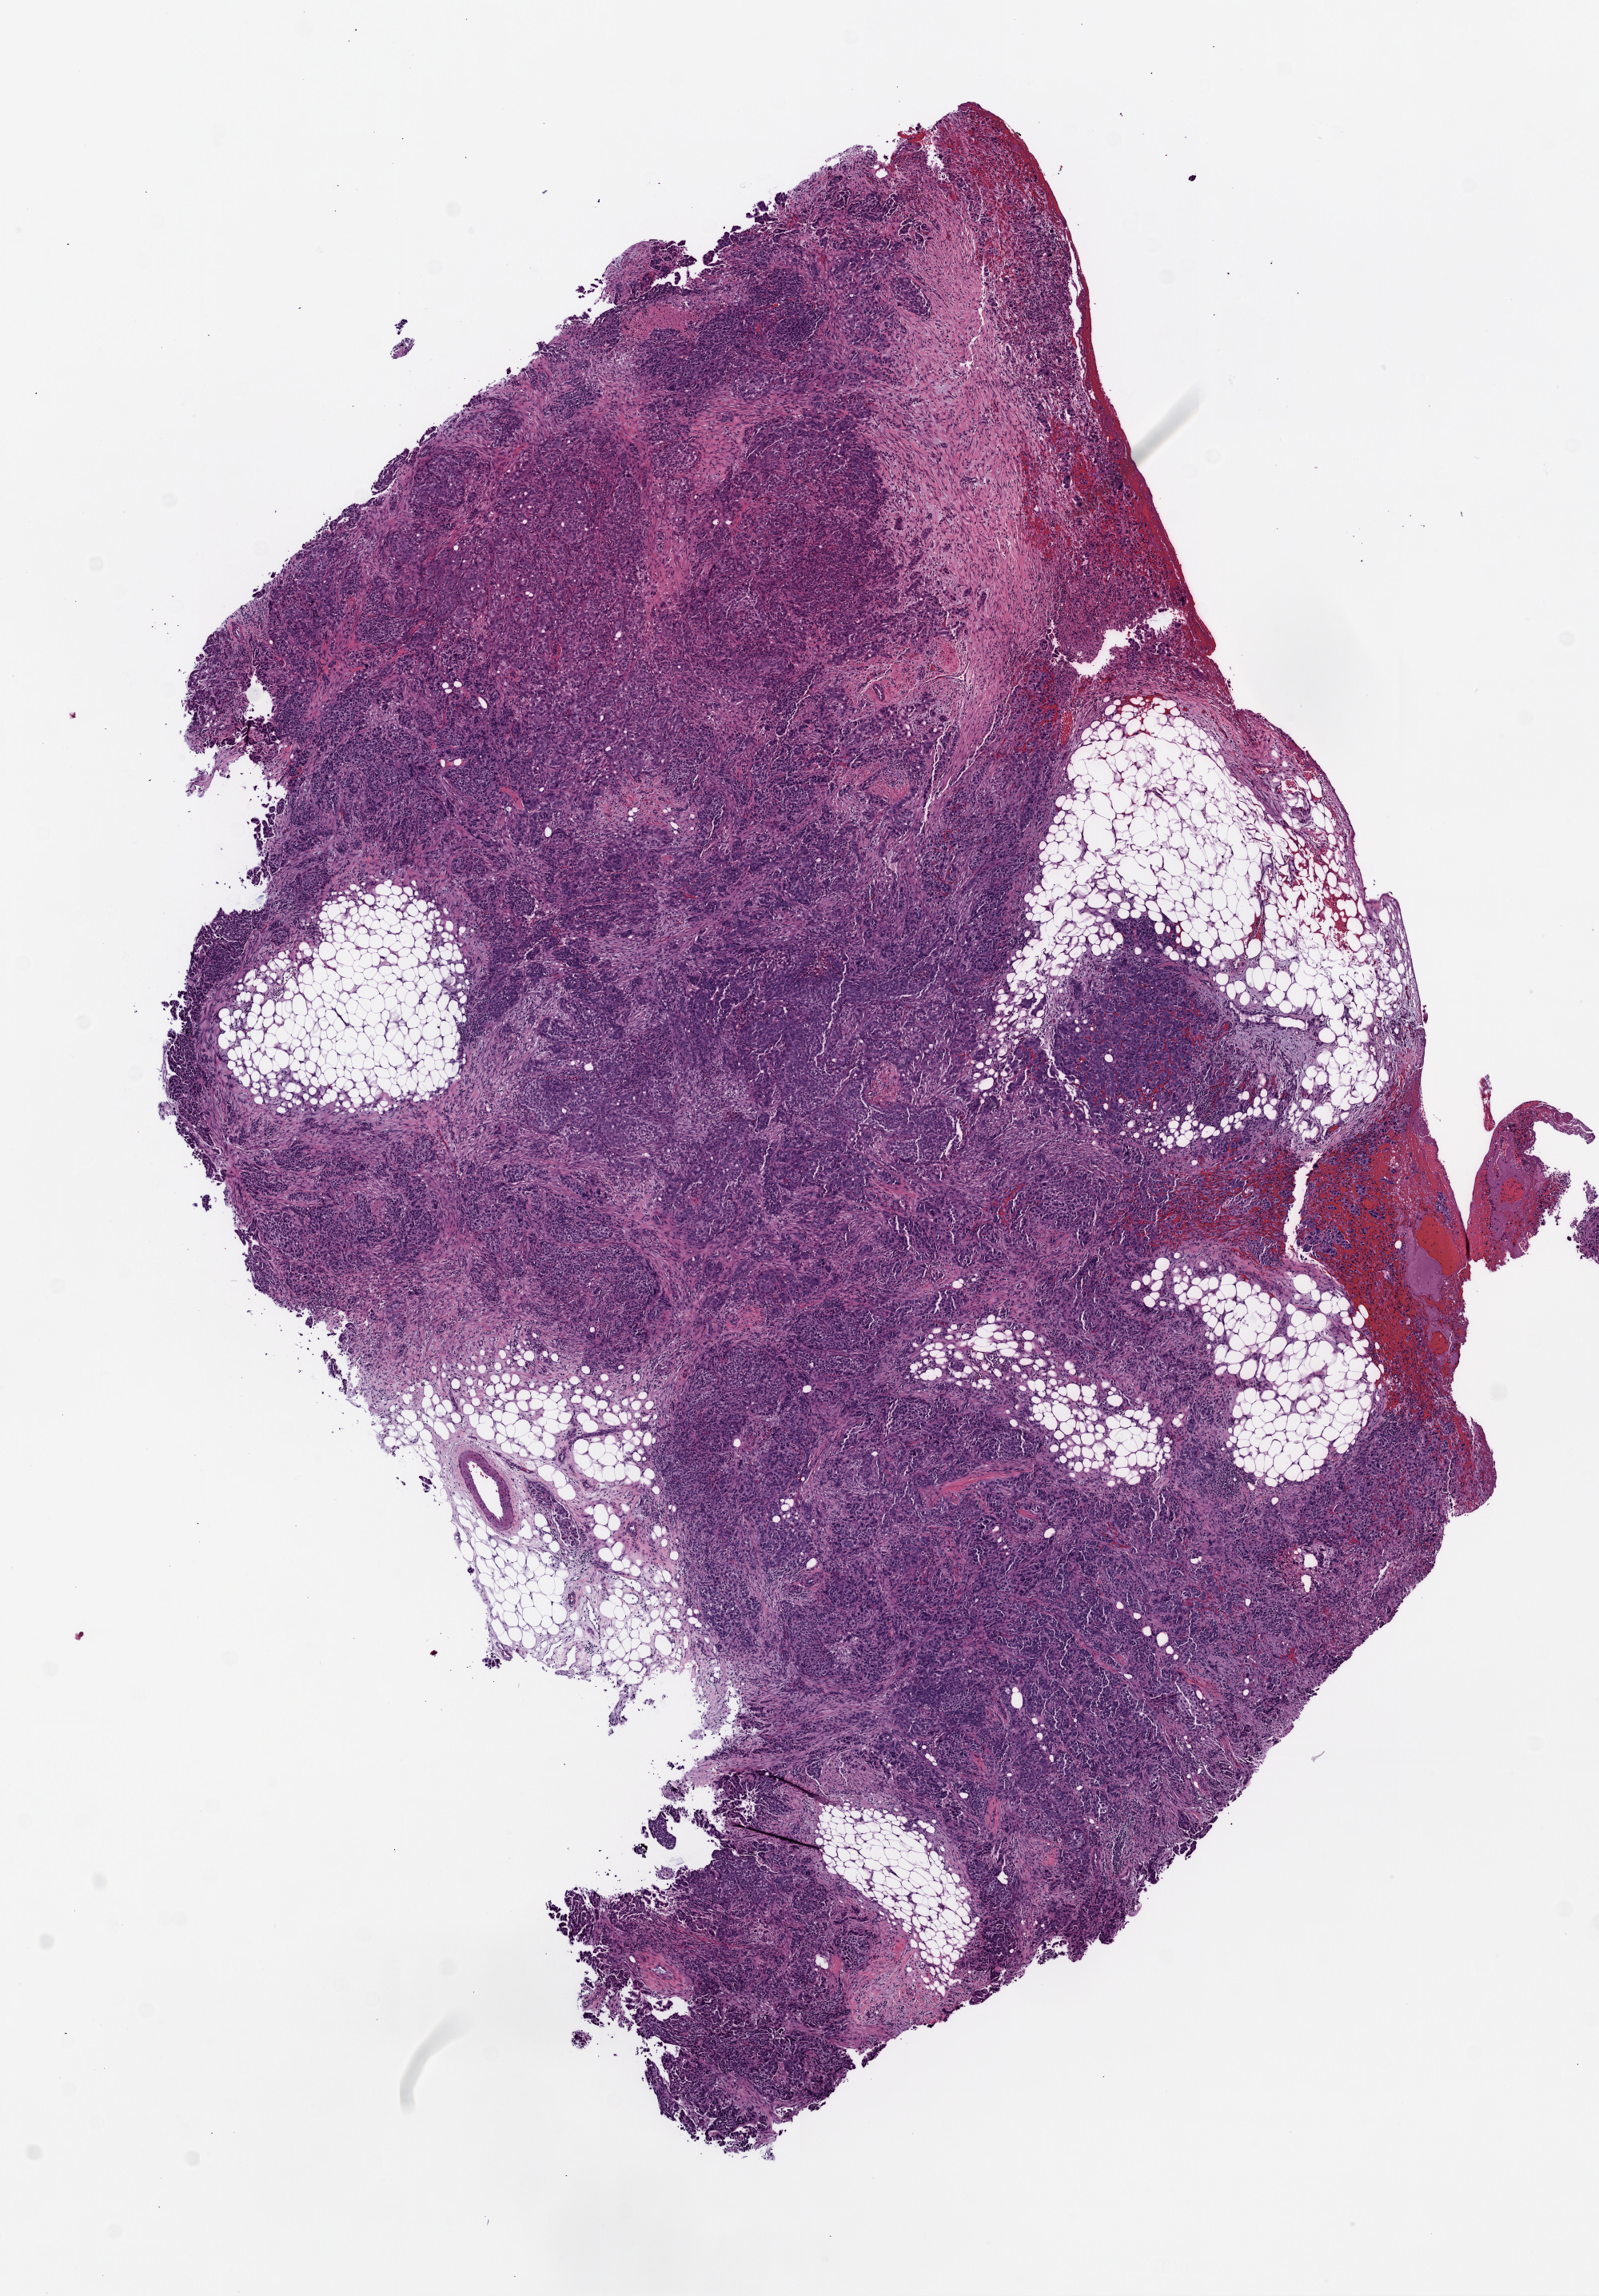
Whole-slide histology image, H&E-stained — shown as a low-resolution overview of the whole scanned area (about 8.0 x 11.5 mm, slide scanned at 20x), frozen section from the top of the tissue portion, primary tumour sample from the ovary. Patient: female, age at initial diagnosis 61 years. Histologic grade: G3 (poorly differentiated). Slide review estimates, as recorded: tumour cells 85%, tumour nuclei 80%, normal cells 15%, stromal cells 0%, necrosis 0%.
FIGO stage: IV. Diagnosis: Serous cystadenocarcinoma, NOS.